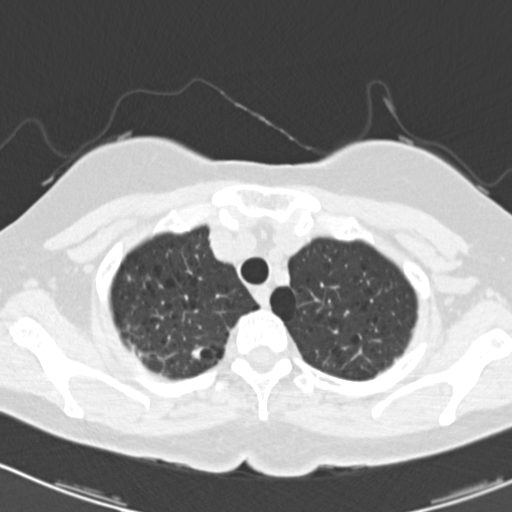
Axial slice from a low-dose chest CT screening exam, baseline screening round, lung window (W 1500 / L -600 HU), 2 mm slice thickness, 120 kVp, slice 26 of 166 in the series. Female participant, aged 64 years at enrolment. Current smoker at enrolment.
Expert-annotated lung lesion, bounding box (x1, y1, x2, y2) in pixels: (180, 335, 226, 372). Screening reader's record for this exam: no non-calcified nodule ≥4 mm recorded. Official screen result: negative screen, minor abnormalities not suspicious for lung cancer. Participant outcome: lung cancer diagnosed 402 days after this screen (after the second annual screen) — adenocarcinoma, NOS, right upper lobe, poorly differentiated (G3), stage IB (AJCC 6th edition), 15 mm at pathology.